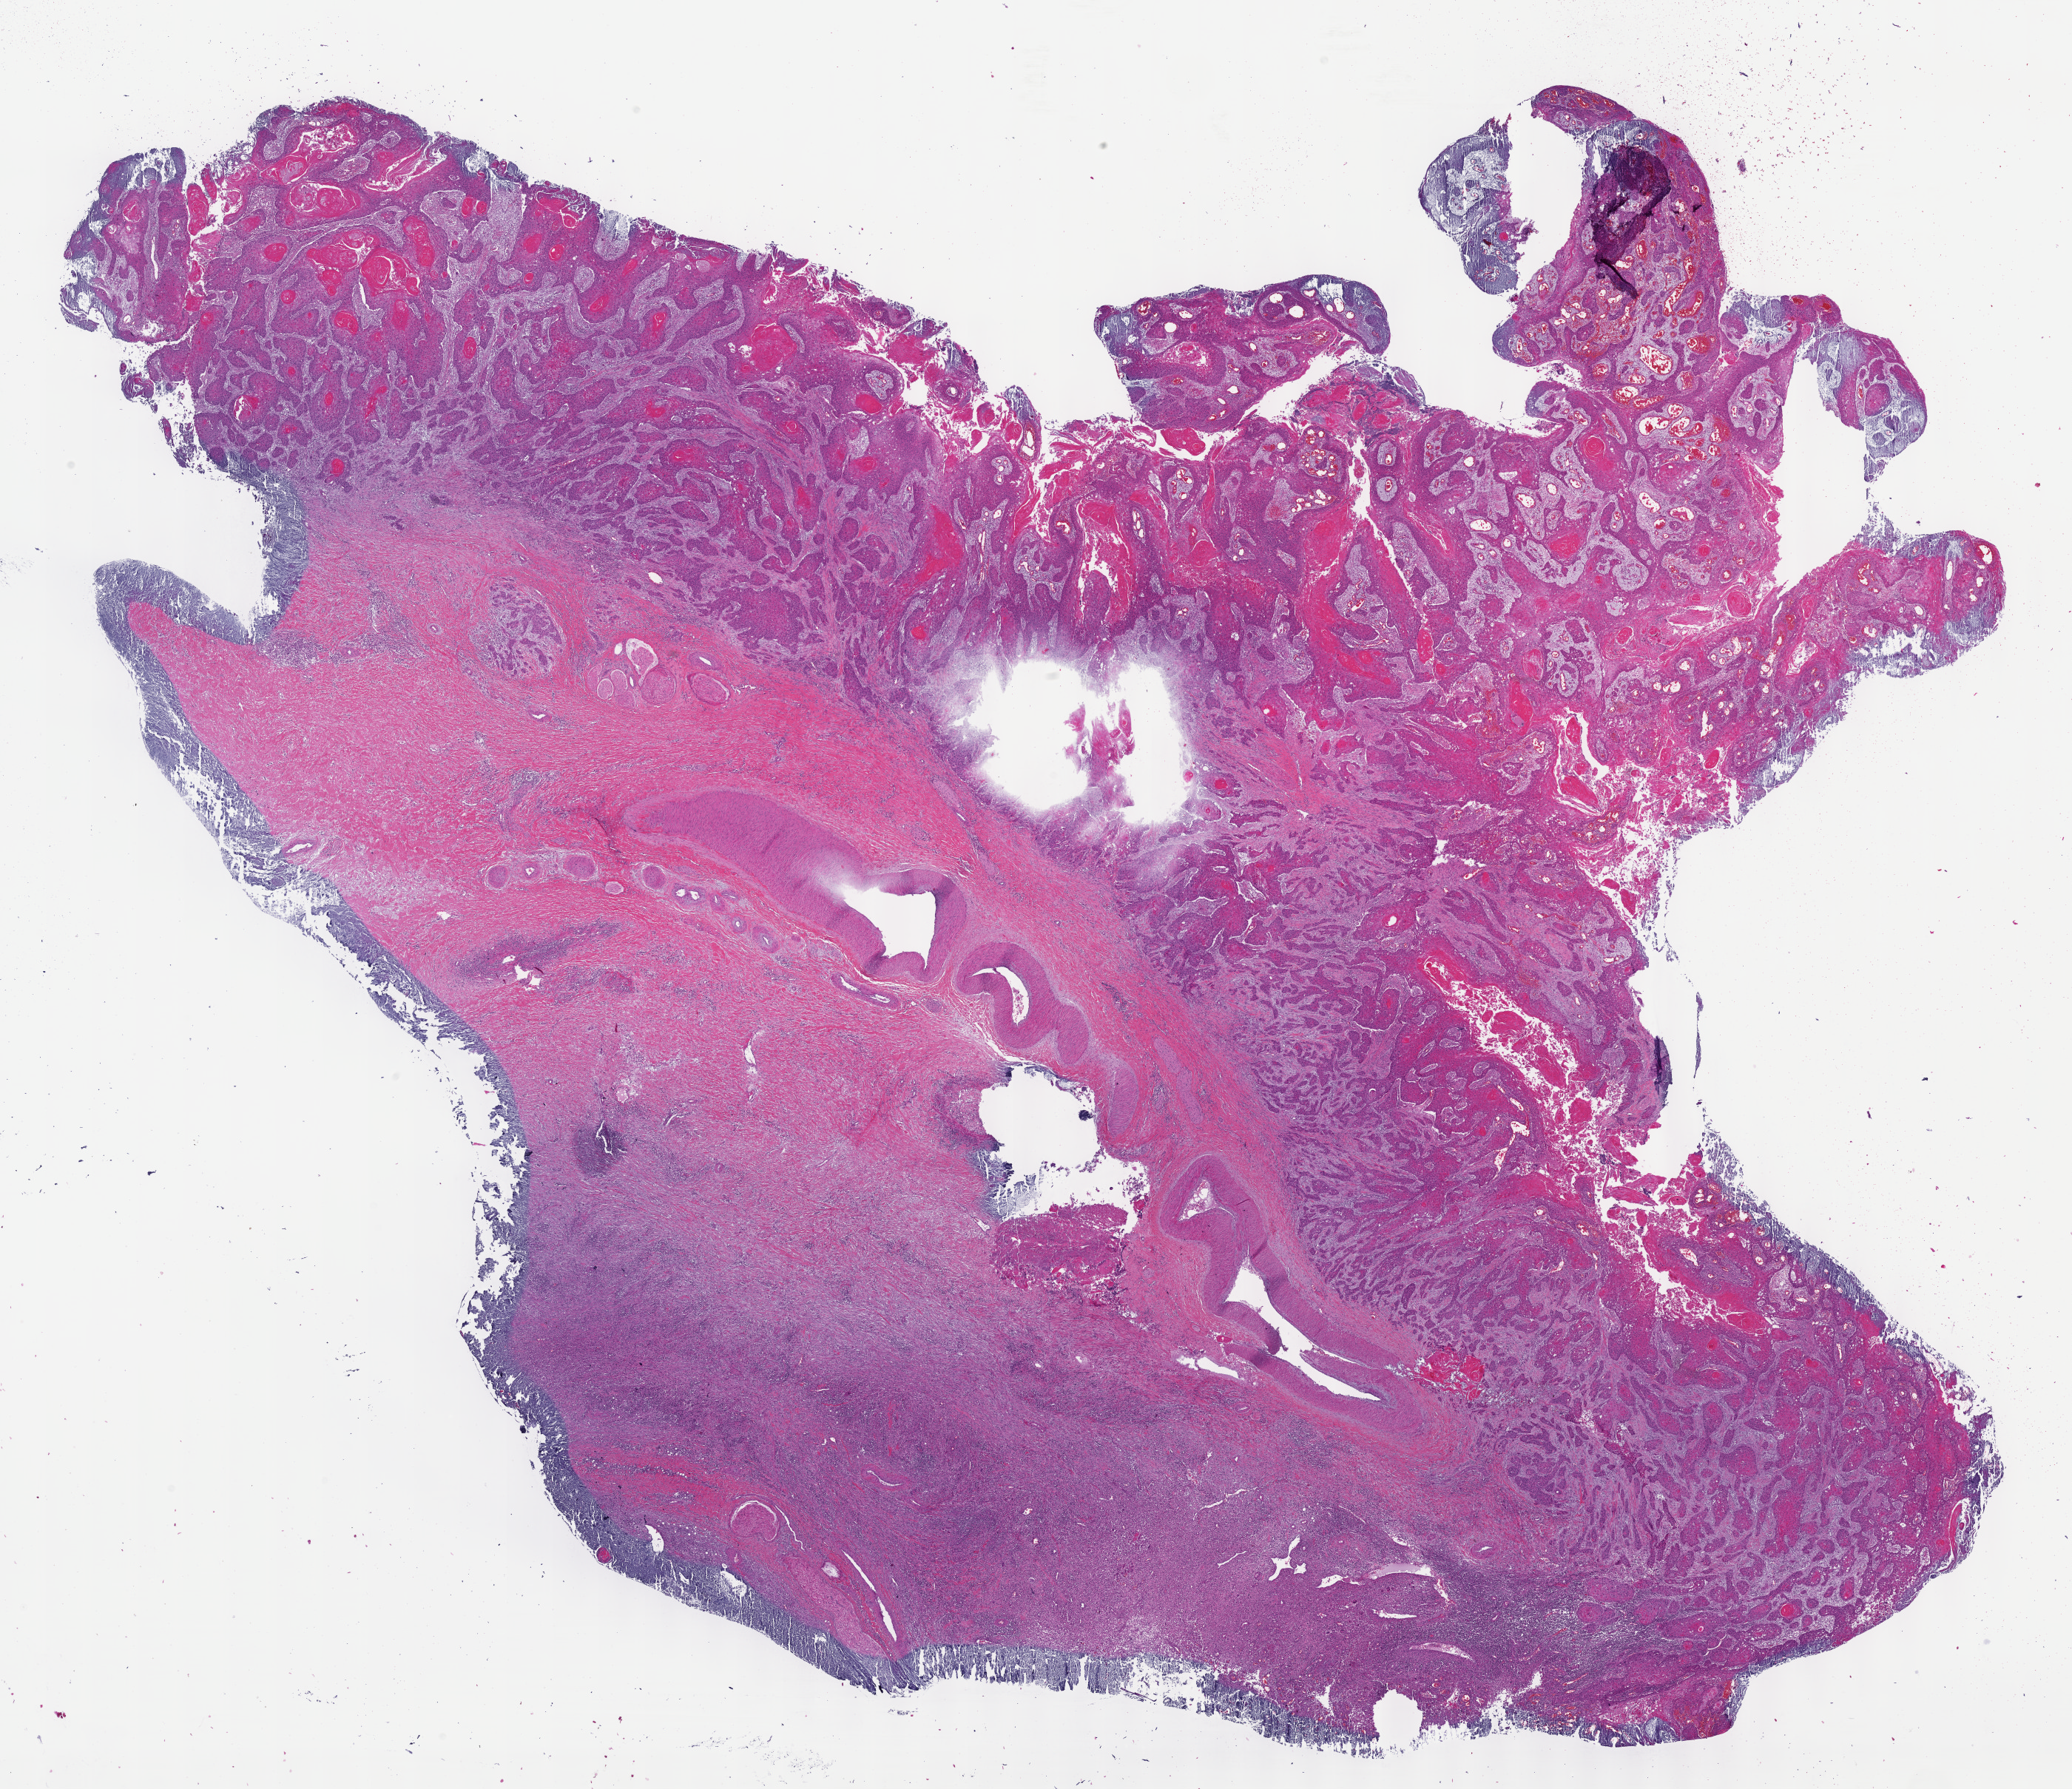
H&E whole-slide image — shown as a low-resolution overview of the whole scanned area (about 22.6 x 19.5 mm, from a 40x scan). Formalin-fixed paraffin-embedded (FFPE) diagnostic section. Head and neck, primary tumour sample. Patient: male, age at initial diagnosis 60 years. Histologic grade: G2 (moderately differentiated).
AJCC pathologic stage: IVA (7th edition). Lymph nodes positive (case pathology): 16 of 82 examined. Histologic diagnosis: Squamous cell carcinoma, NOS (larynx, NOS).